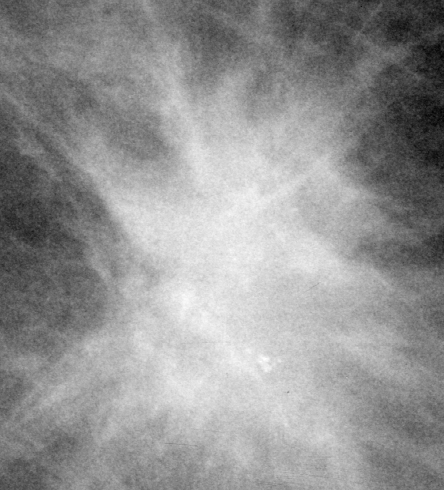
Crop from a digitized film mammogram around one marked abnormality; left breast; CC view; BI-RADS breast density category 2 (scale 1–4).
- Marked abnormality: mass, shape irregular / architectural distortion, margins spiculated; BI-RADS assessment category 5; pathology result (as recorded, not read from the image): malignant.